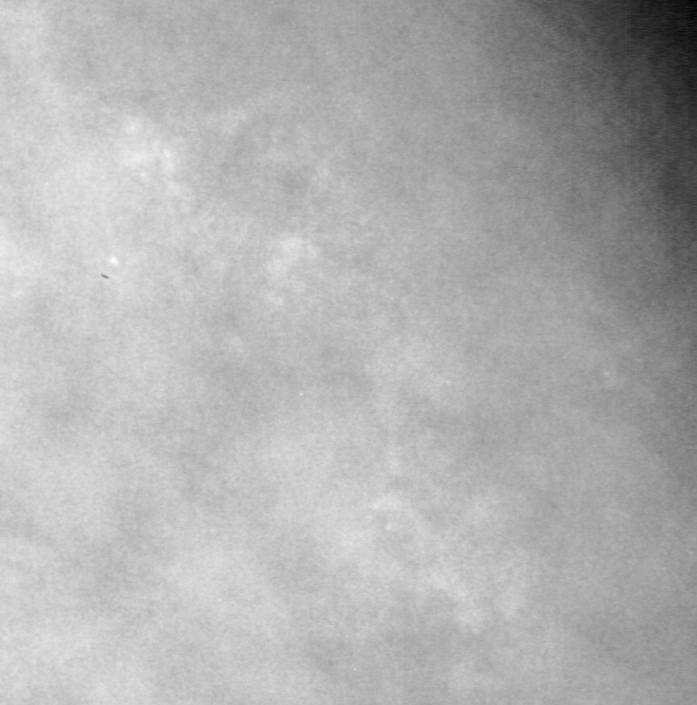
Region of interest cut from a scanned film mammogram (one marked finding), right breast, MLO view, BI-RADS breast density category 4 (scale 1–4).
Calcifications, morphology amorphous, distribution segmental; BI-RADS assessment category 4; pathology (as recorded): benign.